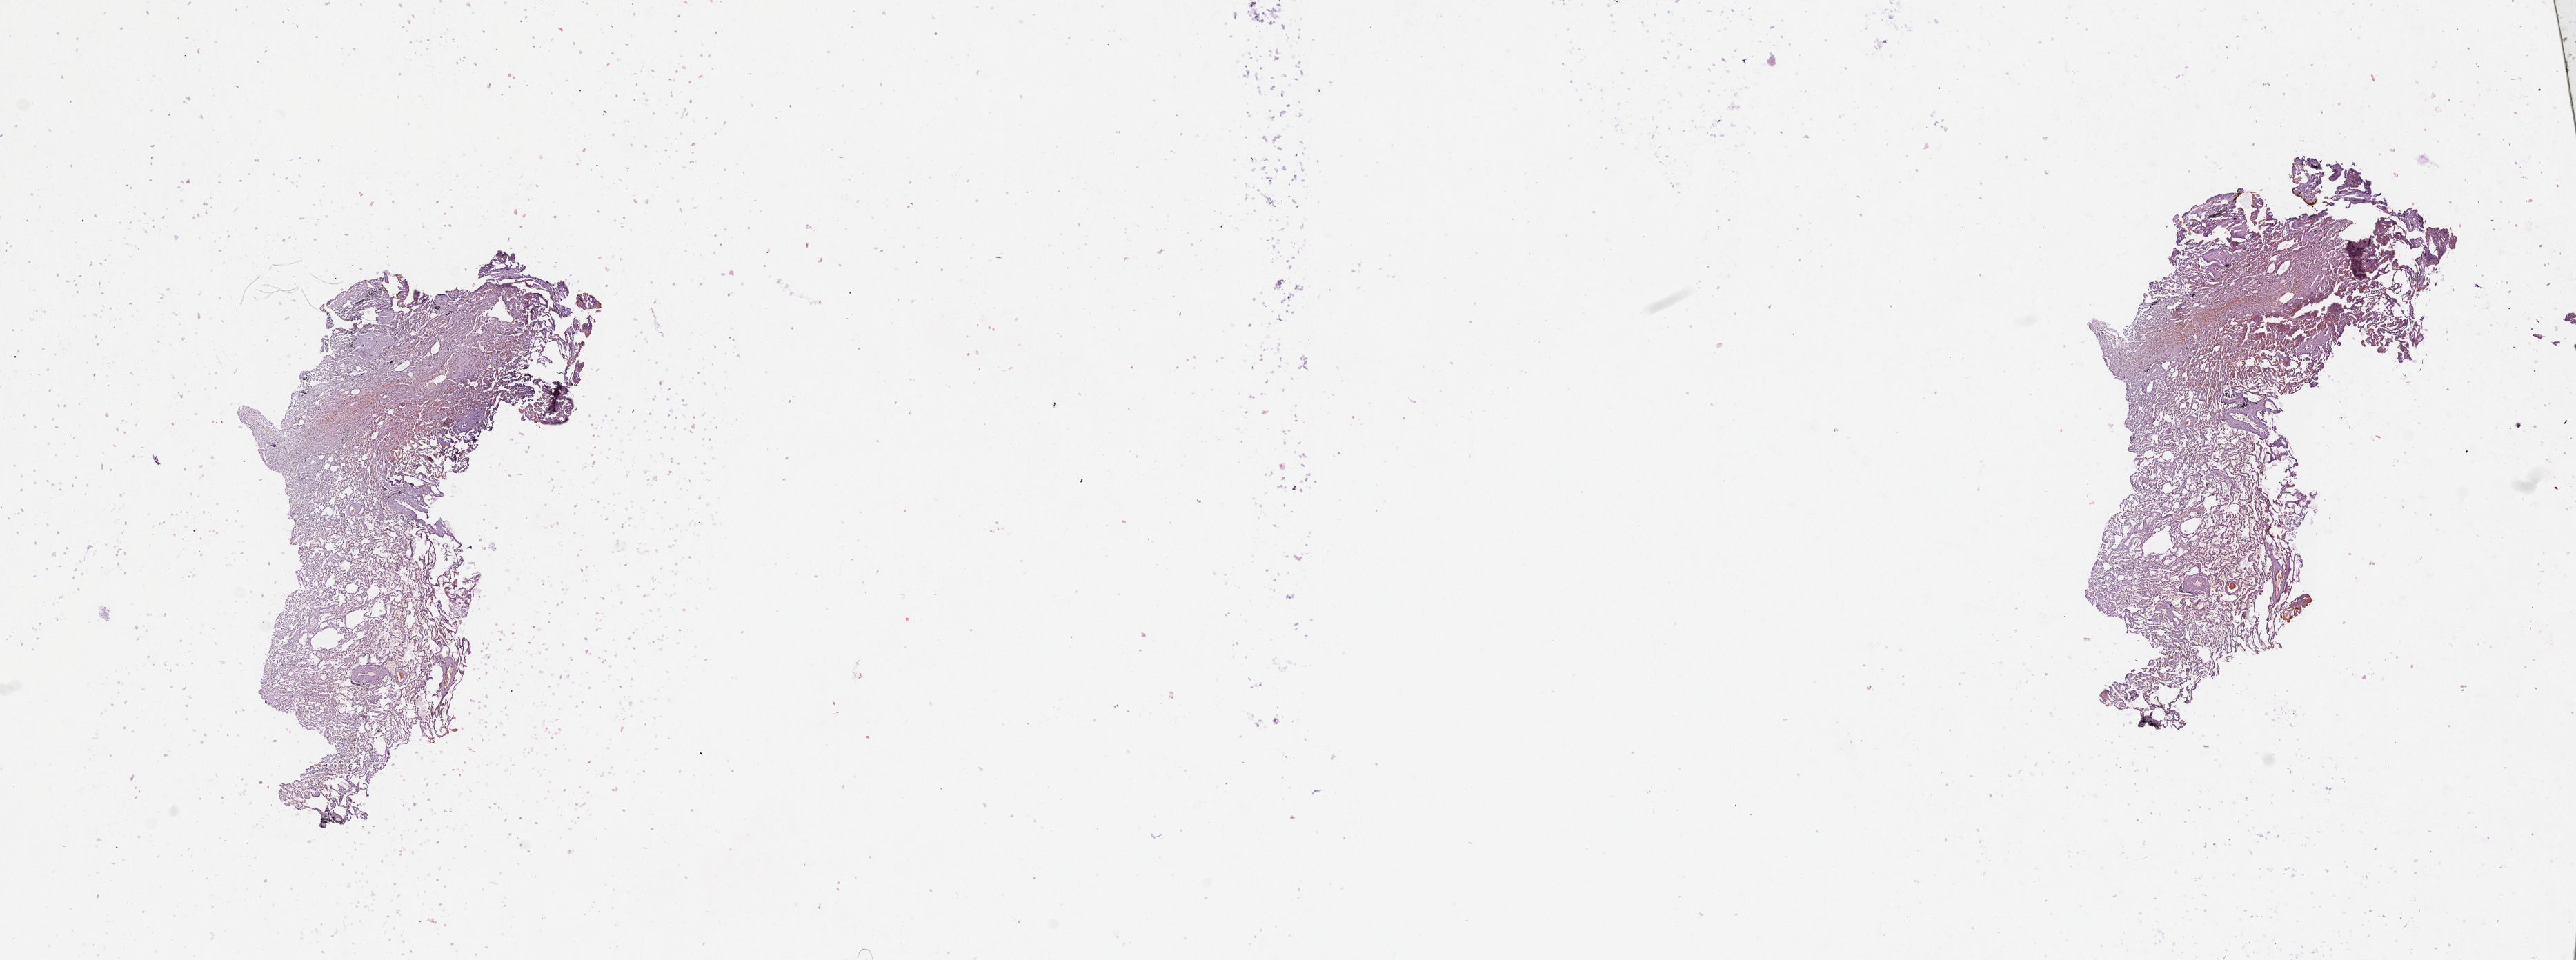
Digitized Hematoxylin and eosin (H&E) stained tissue section (whole slide), shown as a low-resolution overview of the whole scanned area (about 29.5 x 11.0 mm), normal (non-tumour) tissue sample, lung. Male, 74 y/o.
• this section: normal (non-tumour) tissue from the same patient
• patient diagnosis: Squamous cell carcinoma, NOS